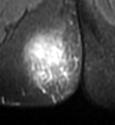
MRI of an extremity soft-tissue mass, one axial slice; position 16 of 49 along the scan axis; STIR; MR volume resampled by the dataset authors to the PET/CT grid (not the native acquisition matrix); 3.27 mm slice thickness; 115 × 125 image matrix, field of view 112 × 122 mm. Female patient. Case-level facts recorded for this patient, not image findings: histological type: epithelioid sarcoma; grade: intermediate; site of the primary tumour: right buttock.
Annotated regions visible in this slice (expert contour drawn on MRI and transferred to this co-registered scan by the dataset authors):
- gross tumour volume including surrounding oedema: box from (x=22, y=25) to (x=80, y=99) px
- gross tumour volume (mass): (x=26, y=34)–(x=66, y=69)